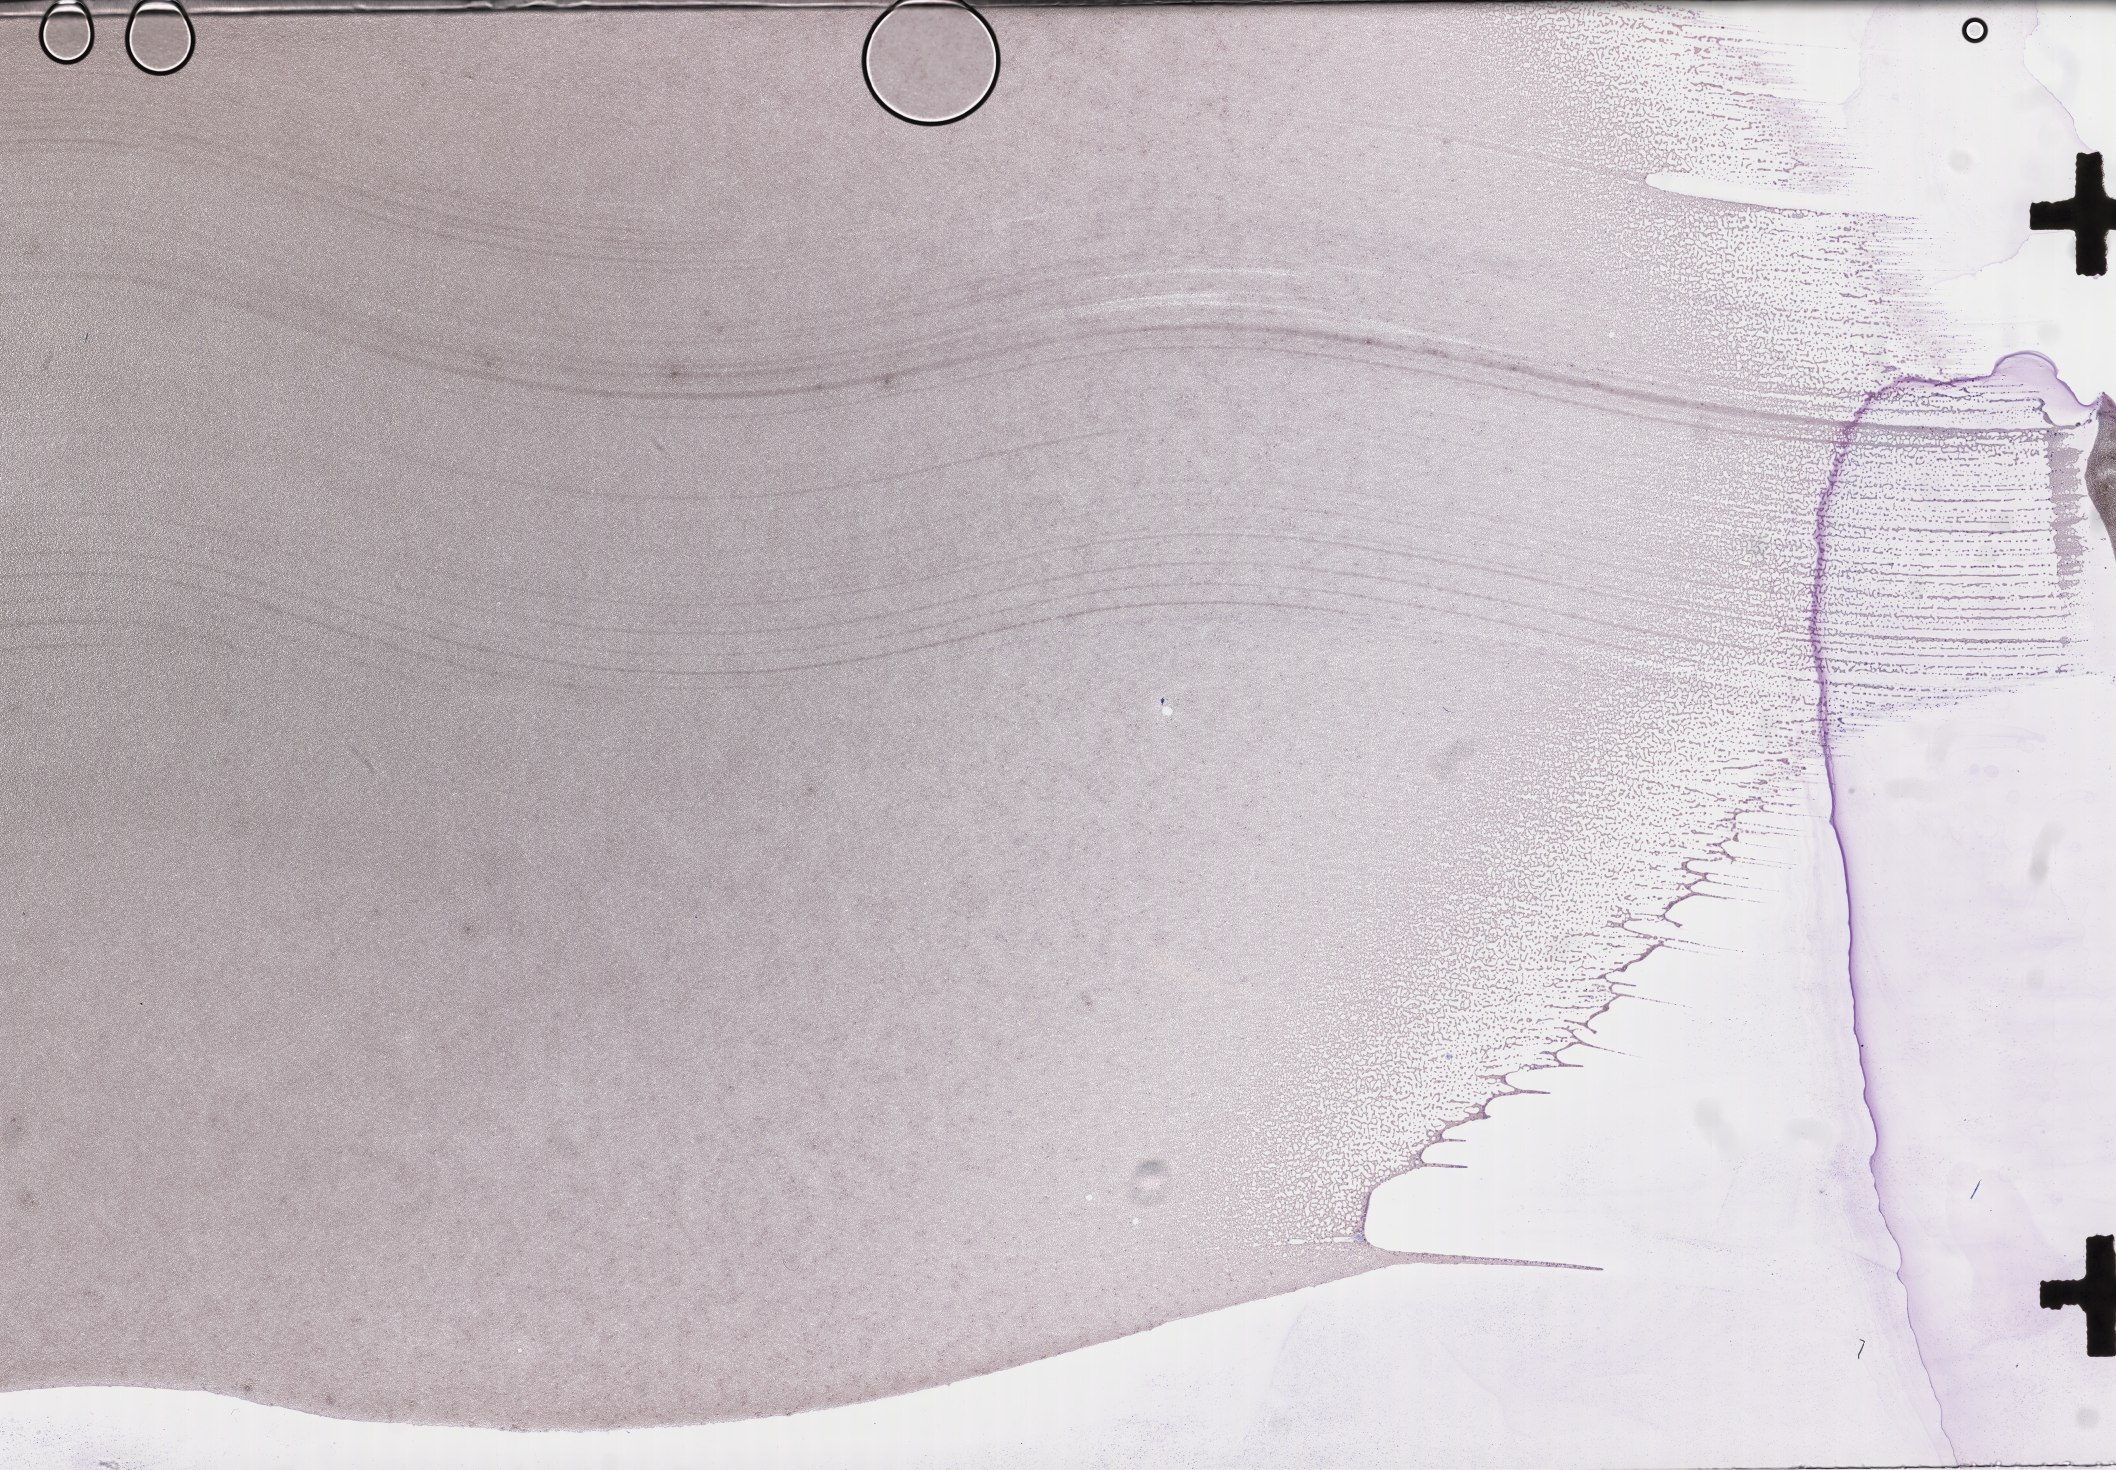
Wright–Giemsa-stained whole blood smear, whole-slide image — low-resolution overview of the scanned area, about 34.2 x 23.7 mm, specimen time point: collected on treatment. Patient sex: male.
- patient diagnosis: Plasma Cell Myeloma